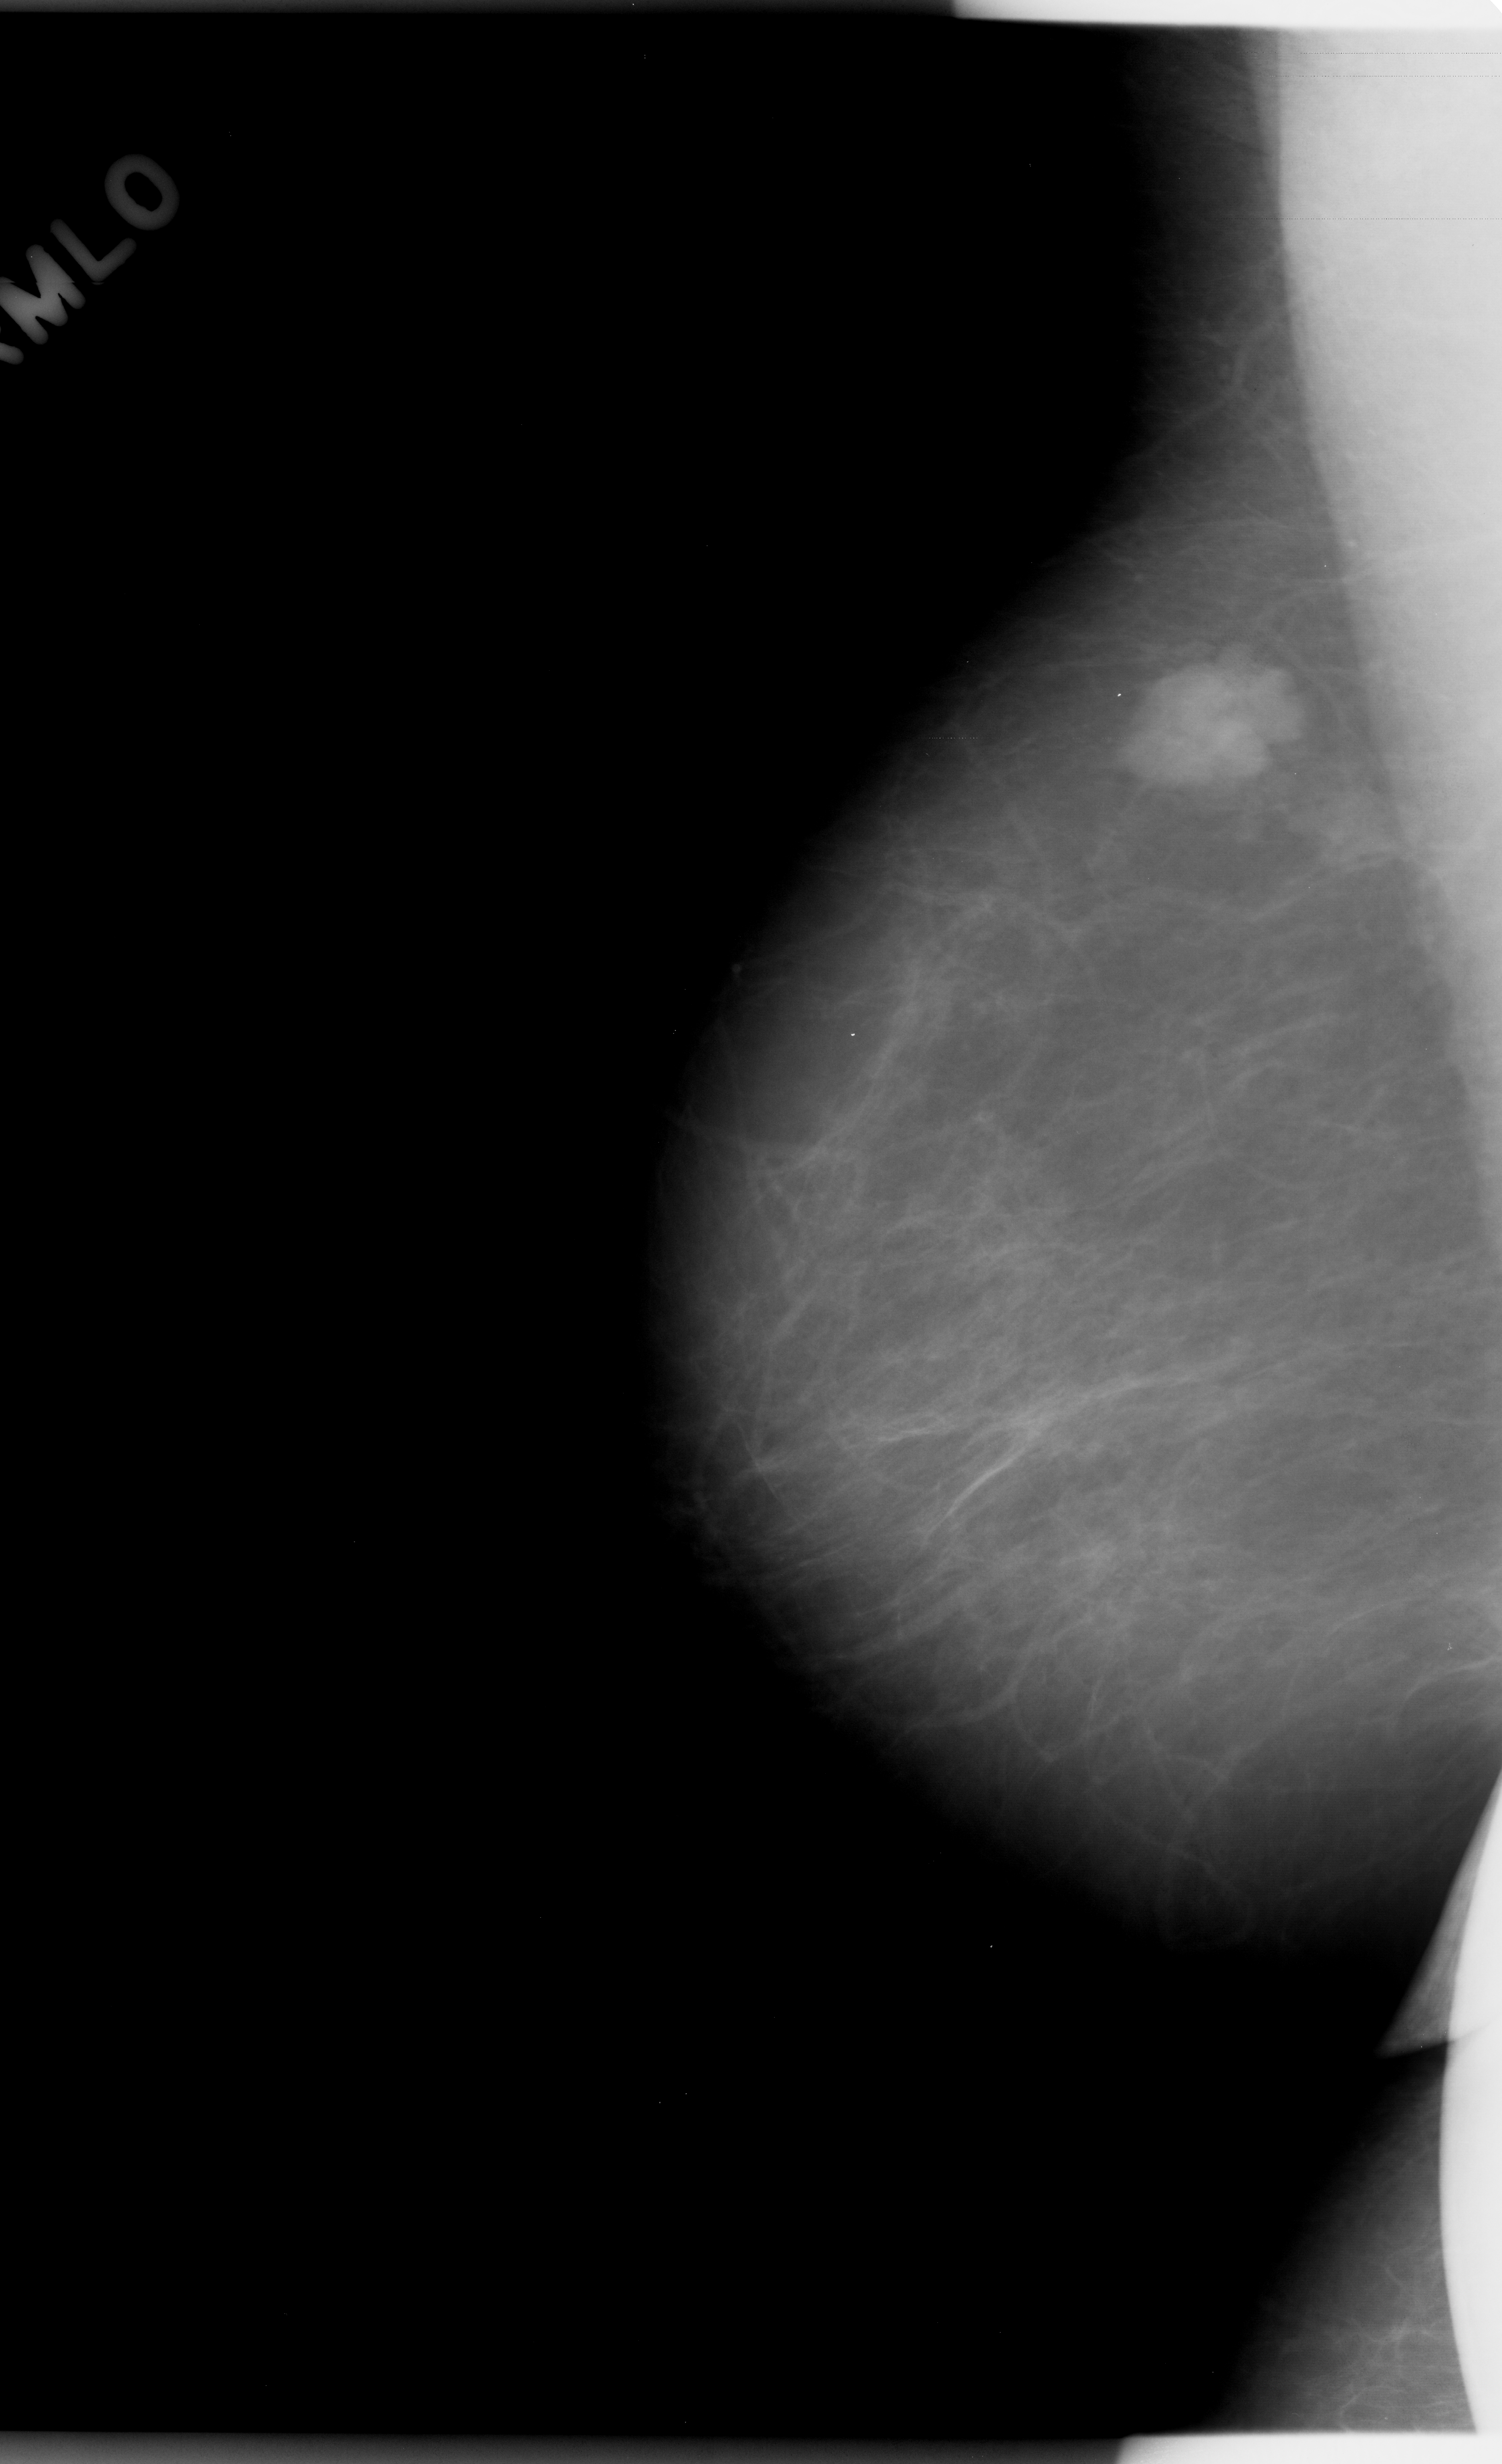
Scanned film-screen mammogram, right breast, mediolateral oblique (MLO) view, breast composition: almost entirely fatty (BI-RADS density category 1 of 4).
Marked findings (only marked abnormalities are described; nothing is implied about the rest of the image): mass, shape lobulated, margins microlobulated; BI-RADS assessment category 5; pathology (as recorded): malignant.